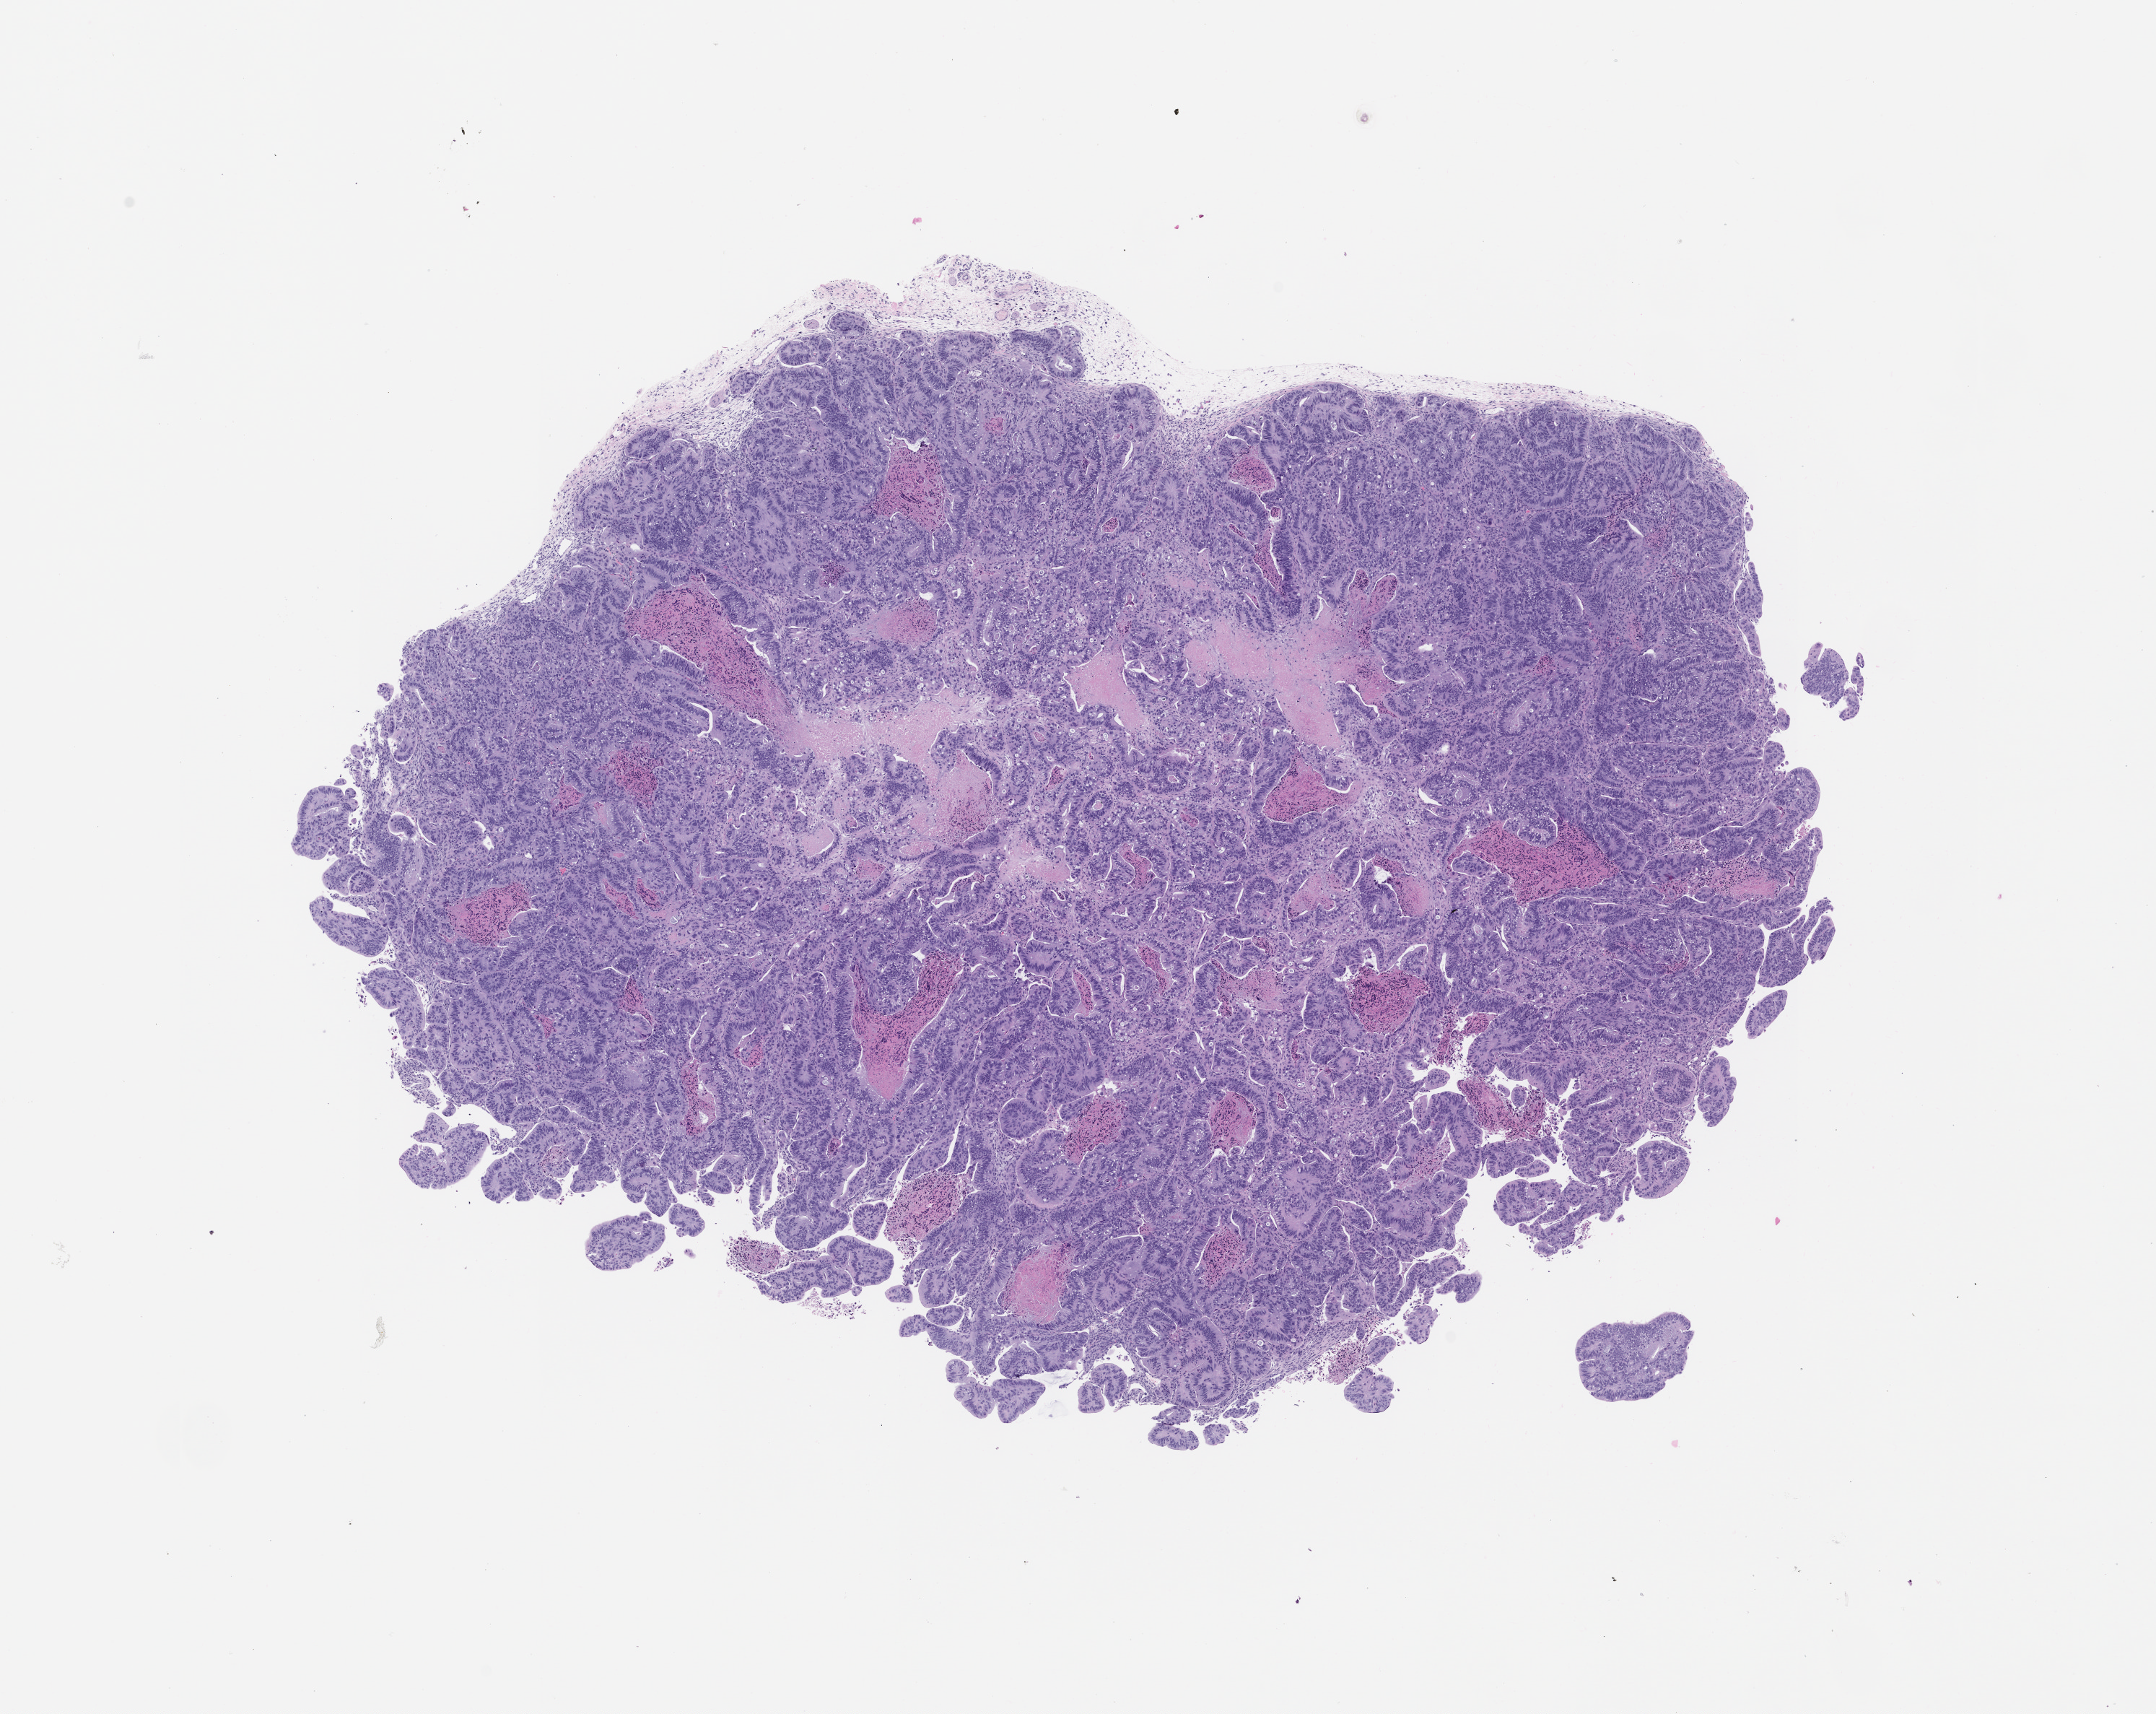
Whole-slide image, hematoxylin and eosin (H&E): patient-derived xenograft (human tumor grown in a mouse), passage 1 — a low-resolution overview of the entire scanned area, about 12.0 x 9.5 mm. Formalin-fixed, paraffin-embedded (FFPE) tissue. Tumor site category: colon.
Originating patient diagnosis: Colon Adenocarcinoma.